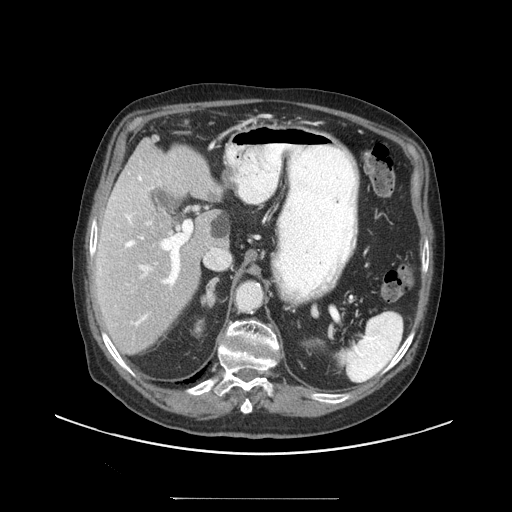
Contrast-enhanced abdominal CT (liver protocol), one axial slice. Position 63 of 97 along the scan axis. 140 kVp. Soft-tissue window (W 400 / L 40 HU). 2.5 mm slice thickness. 512 × 512 image matrix, field of view 450 × 450 mm. Case-level facts recorded for this patient, not image findings: diagnosis: hepatocellular carcinoma (patient treated with transarterial chemoembolisation; whether this scan precedes or follows treatment is not stated here); TNM stage (as recorded): Stage-IIIC; Child-Pugh class: A; tumour differentiation: well differentiated; tumour nodularity: uninodular.
Annotated regions visible in this slice (semi-automatic segmentation, software-assisted and operator-edited):
- liver parenchyma outside the tumour (the mass and vessels are separate outlines, so this box may not span the whole liver): bounding box (x1, y1, x2, y2) in pixels: (94, 136, 228, 354)
- liver vessels: (100, 175, 181, 326)